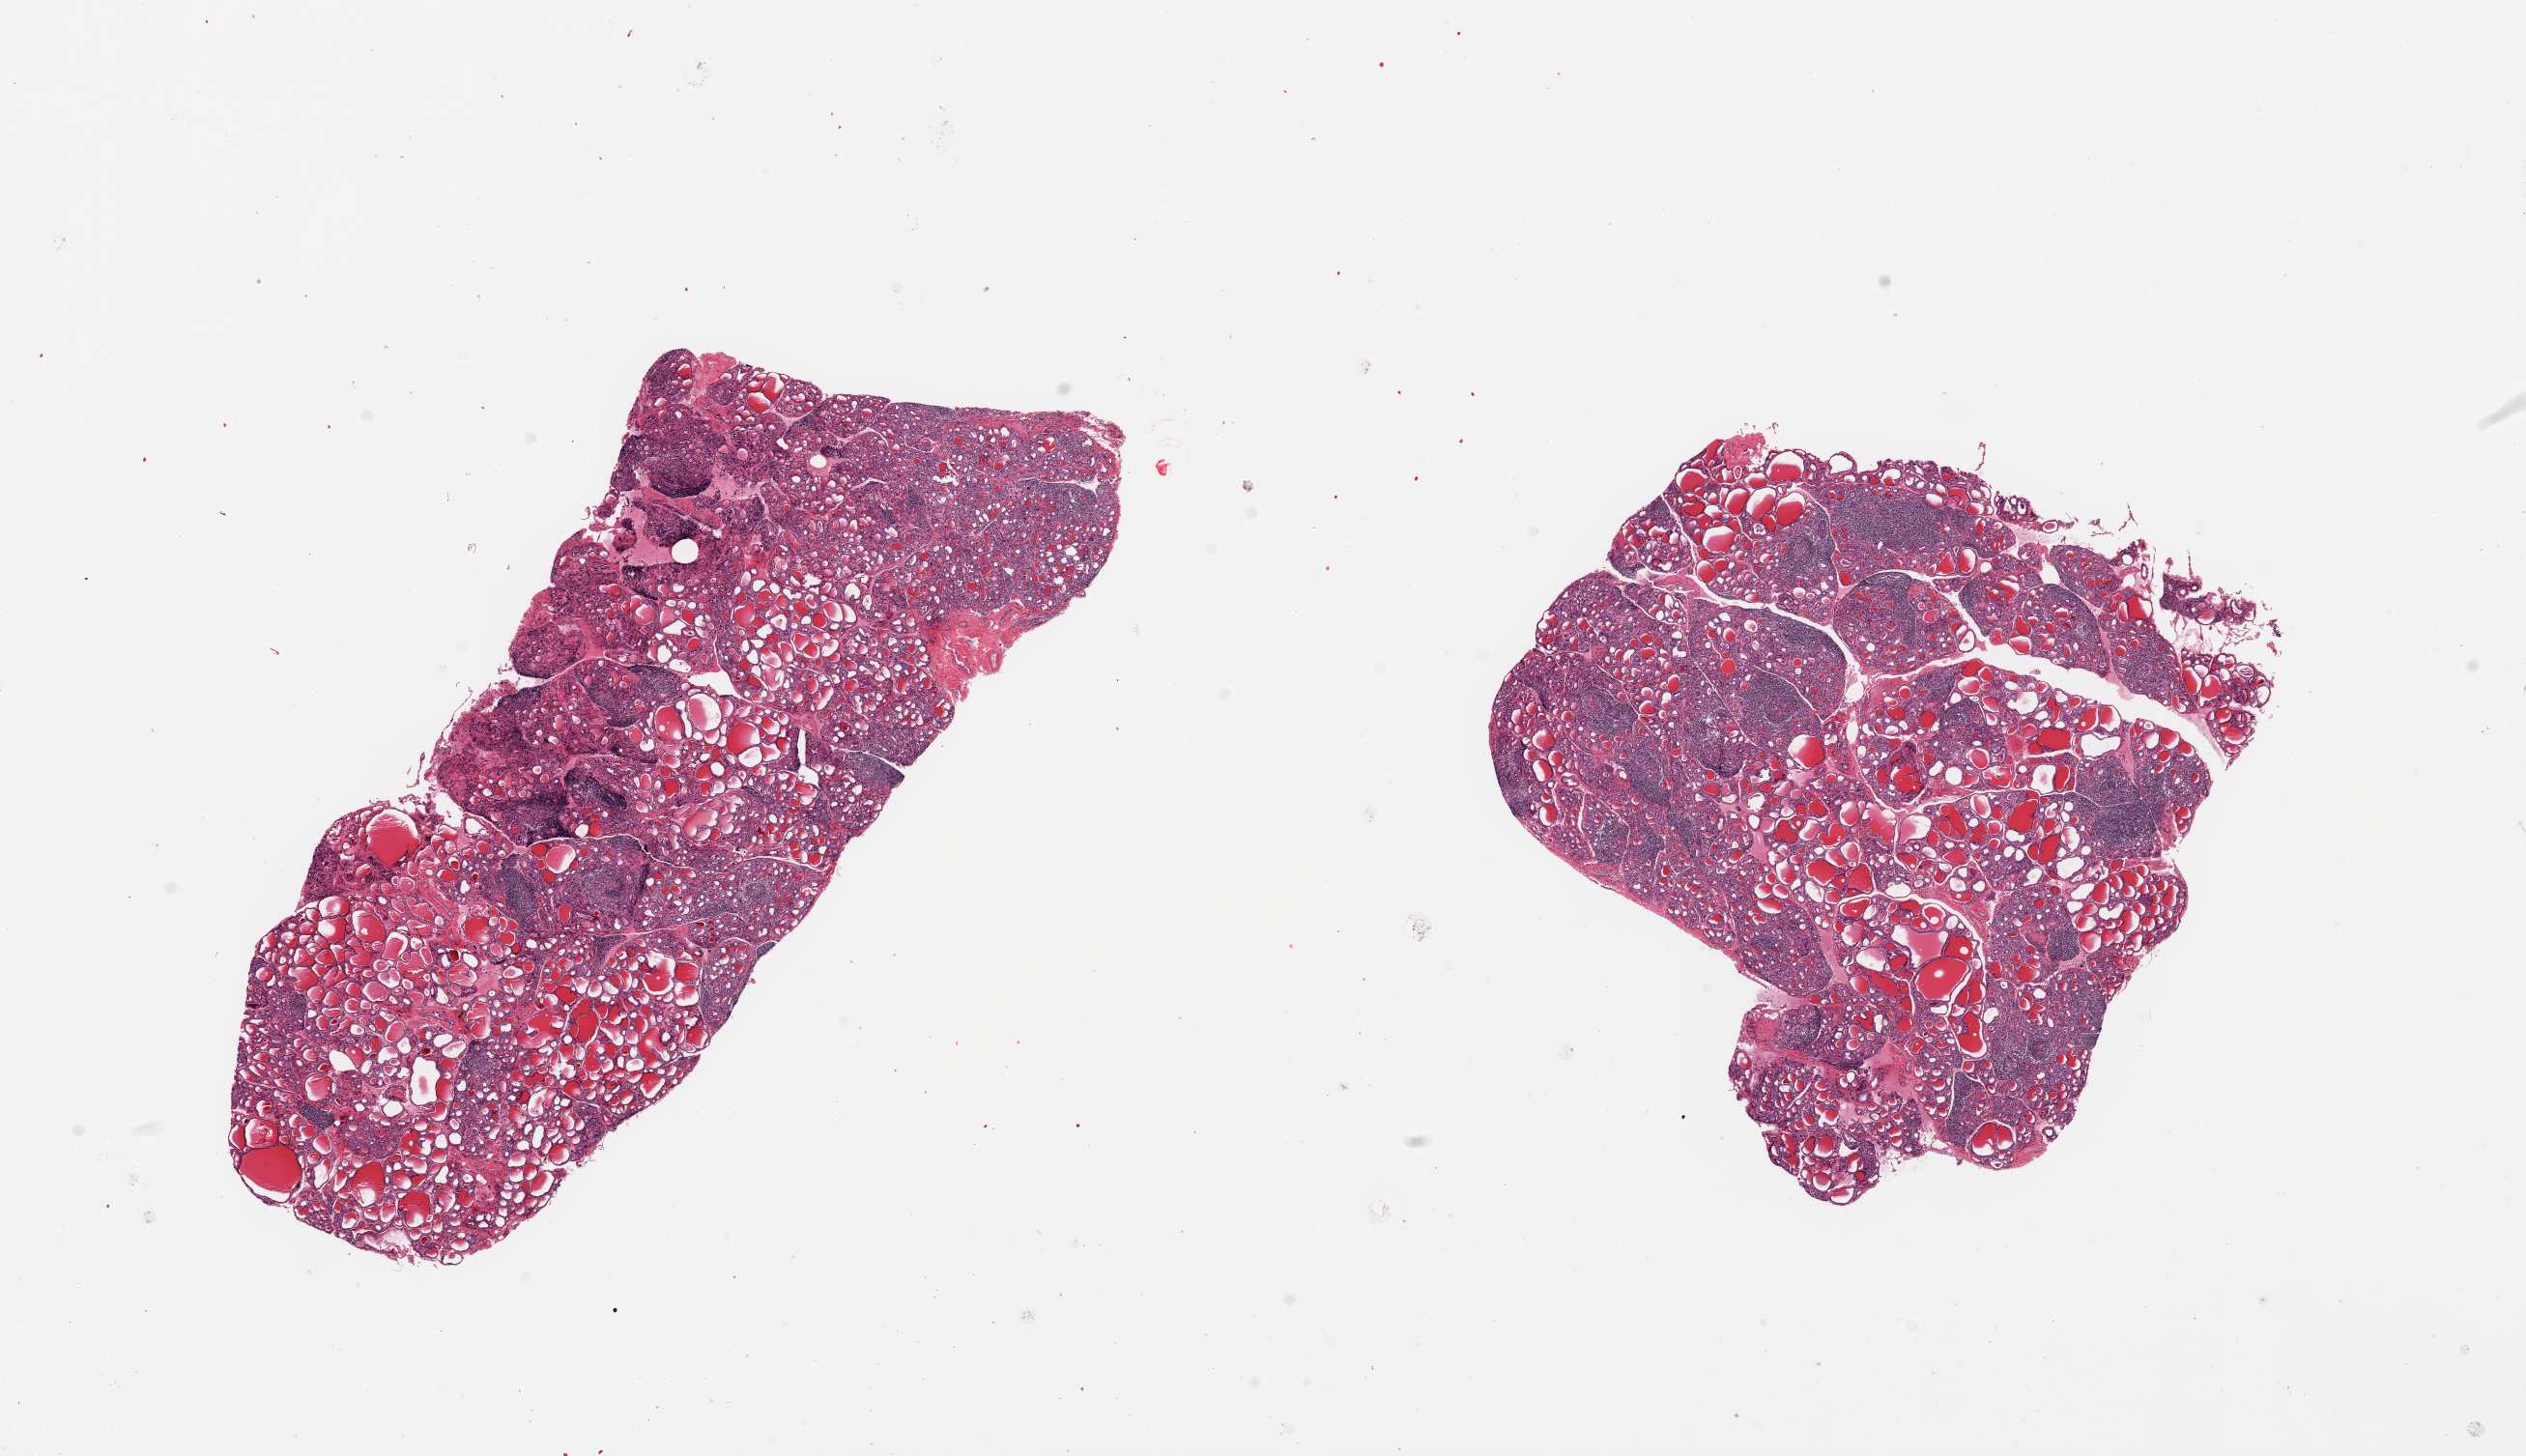
Digitized H&E-stained section, brightfield, a low-resolution overview of the entire scanned area, about 20.7 x 11.9 mm, PAXgene-fixed, paraffin-embedded tissue, sampled site (target tissue): thyroid, donor tissue sample. Donor: male.
Review note (as recorded): 2 pieces; moderate to severe Hashimoto thyroiditis.